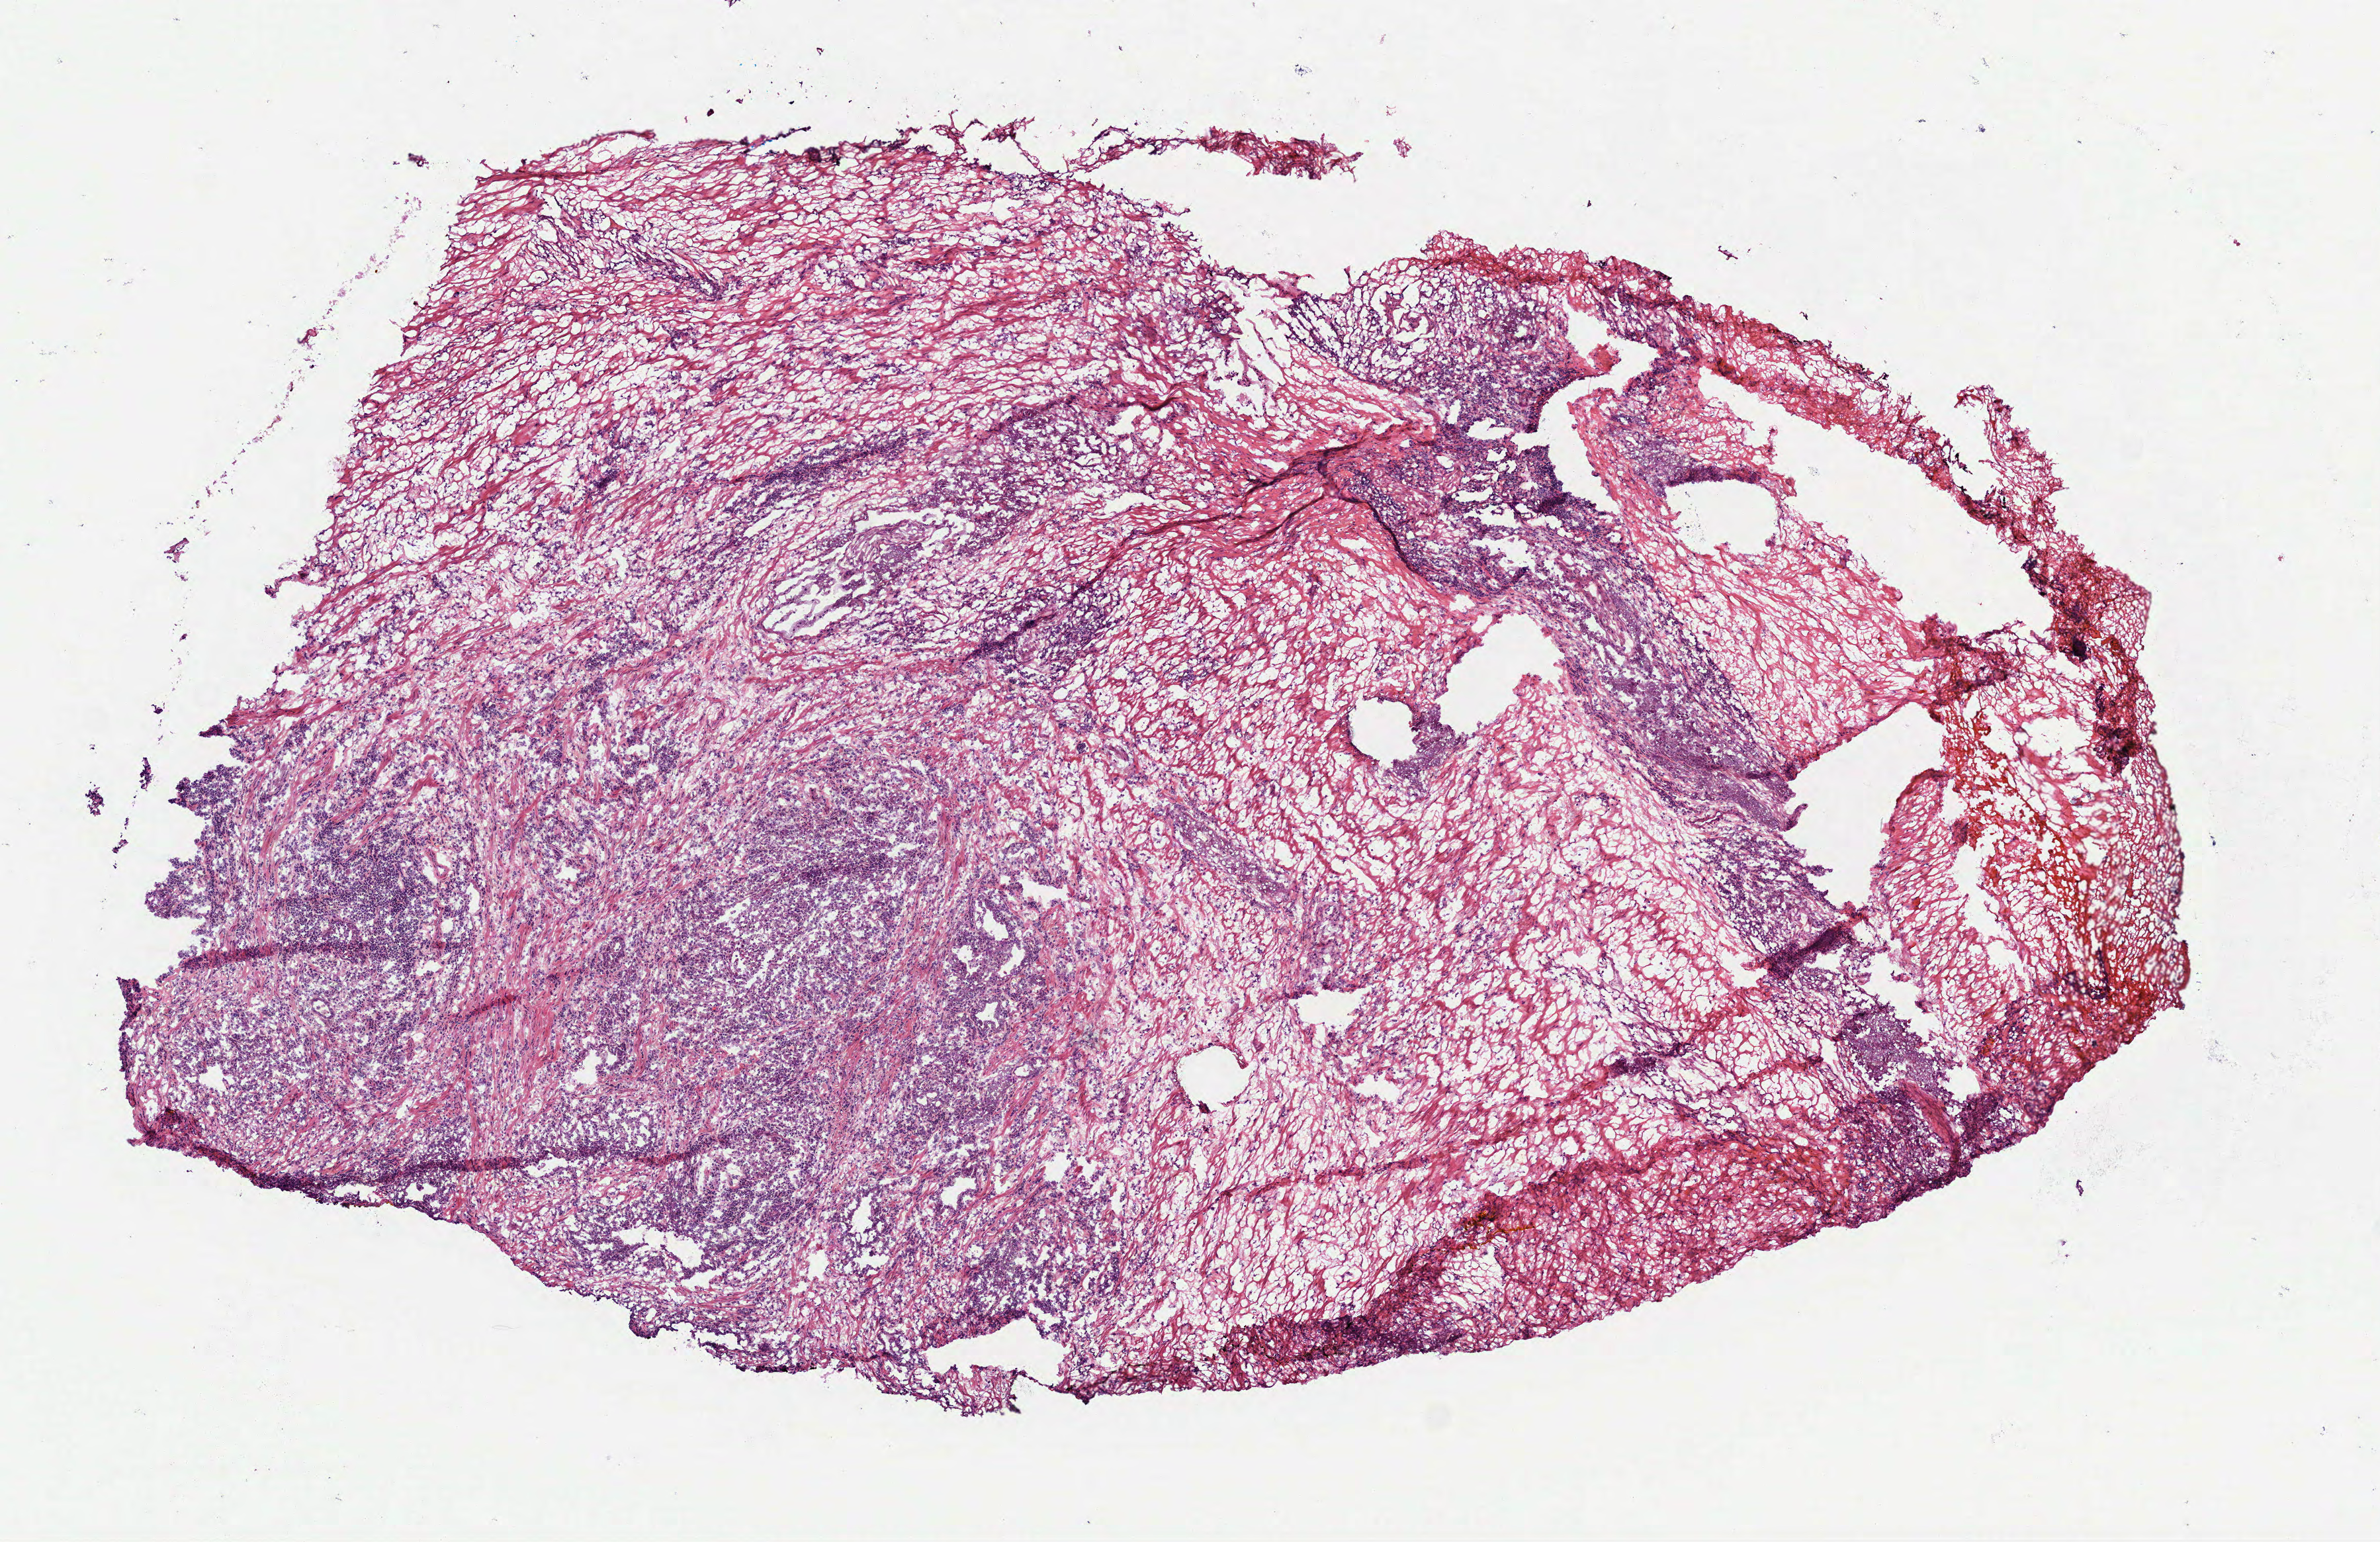
H&E-stained whole-slide image, whole scanned area (about 7.3 x 4.7 mm, acquisition: 40x scan) shown as a low-resolution overview; frozen section from the bottom of the tissue portion; prostate, primary tumour sample. Male, age 51 years at initial diagnosis. Gleason score: 7 (3+4). Pathologist review of this section (percent, as recorded): tumour cells 50%, tumour nuclei 50%, normal cells 5%, stromal cells 45%, necrosis 0%.
Laterality: bilateral. Pathologic diagnosis: Acinar cell carcinoma (prostate gland). Lymph nodes positive (case pathology): 0 of 4 examined.